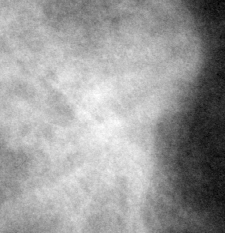
Cropped region of a digitized screen-film mammogram centred on a radiologist-marked abnormality, left breast, MLO view.
- Marked abnormality: mass, shape oval, margins microlobulated; BI-RADS assessment category 4; pathology (as recorded): malignant.